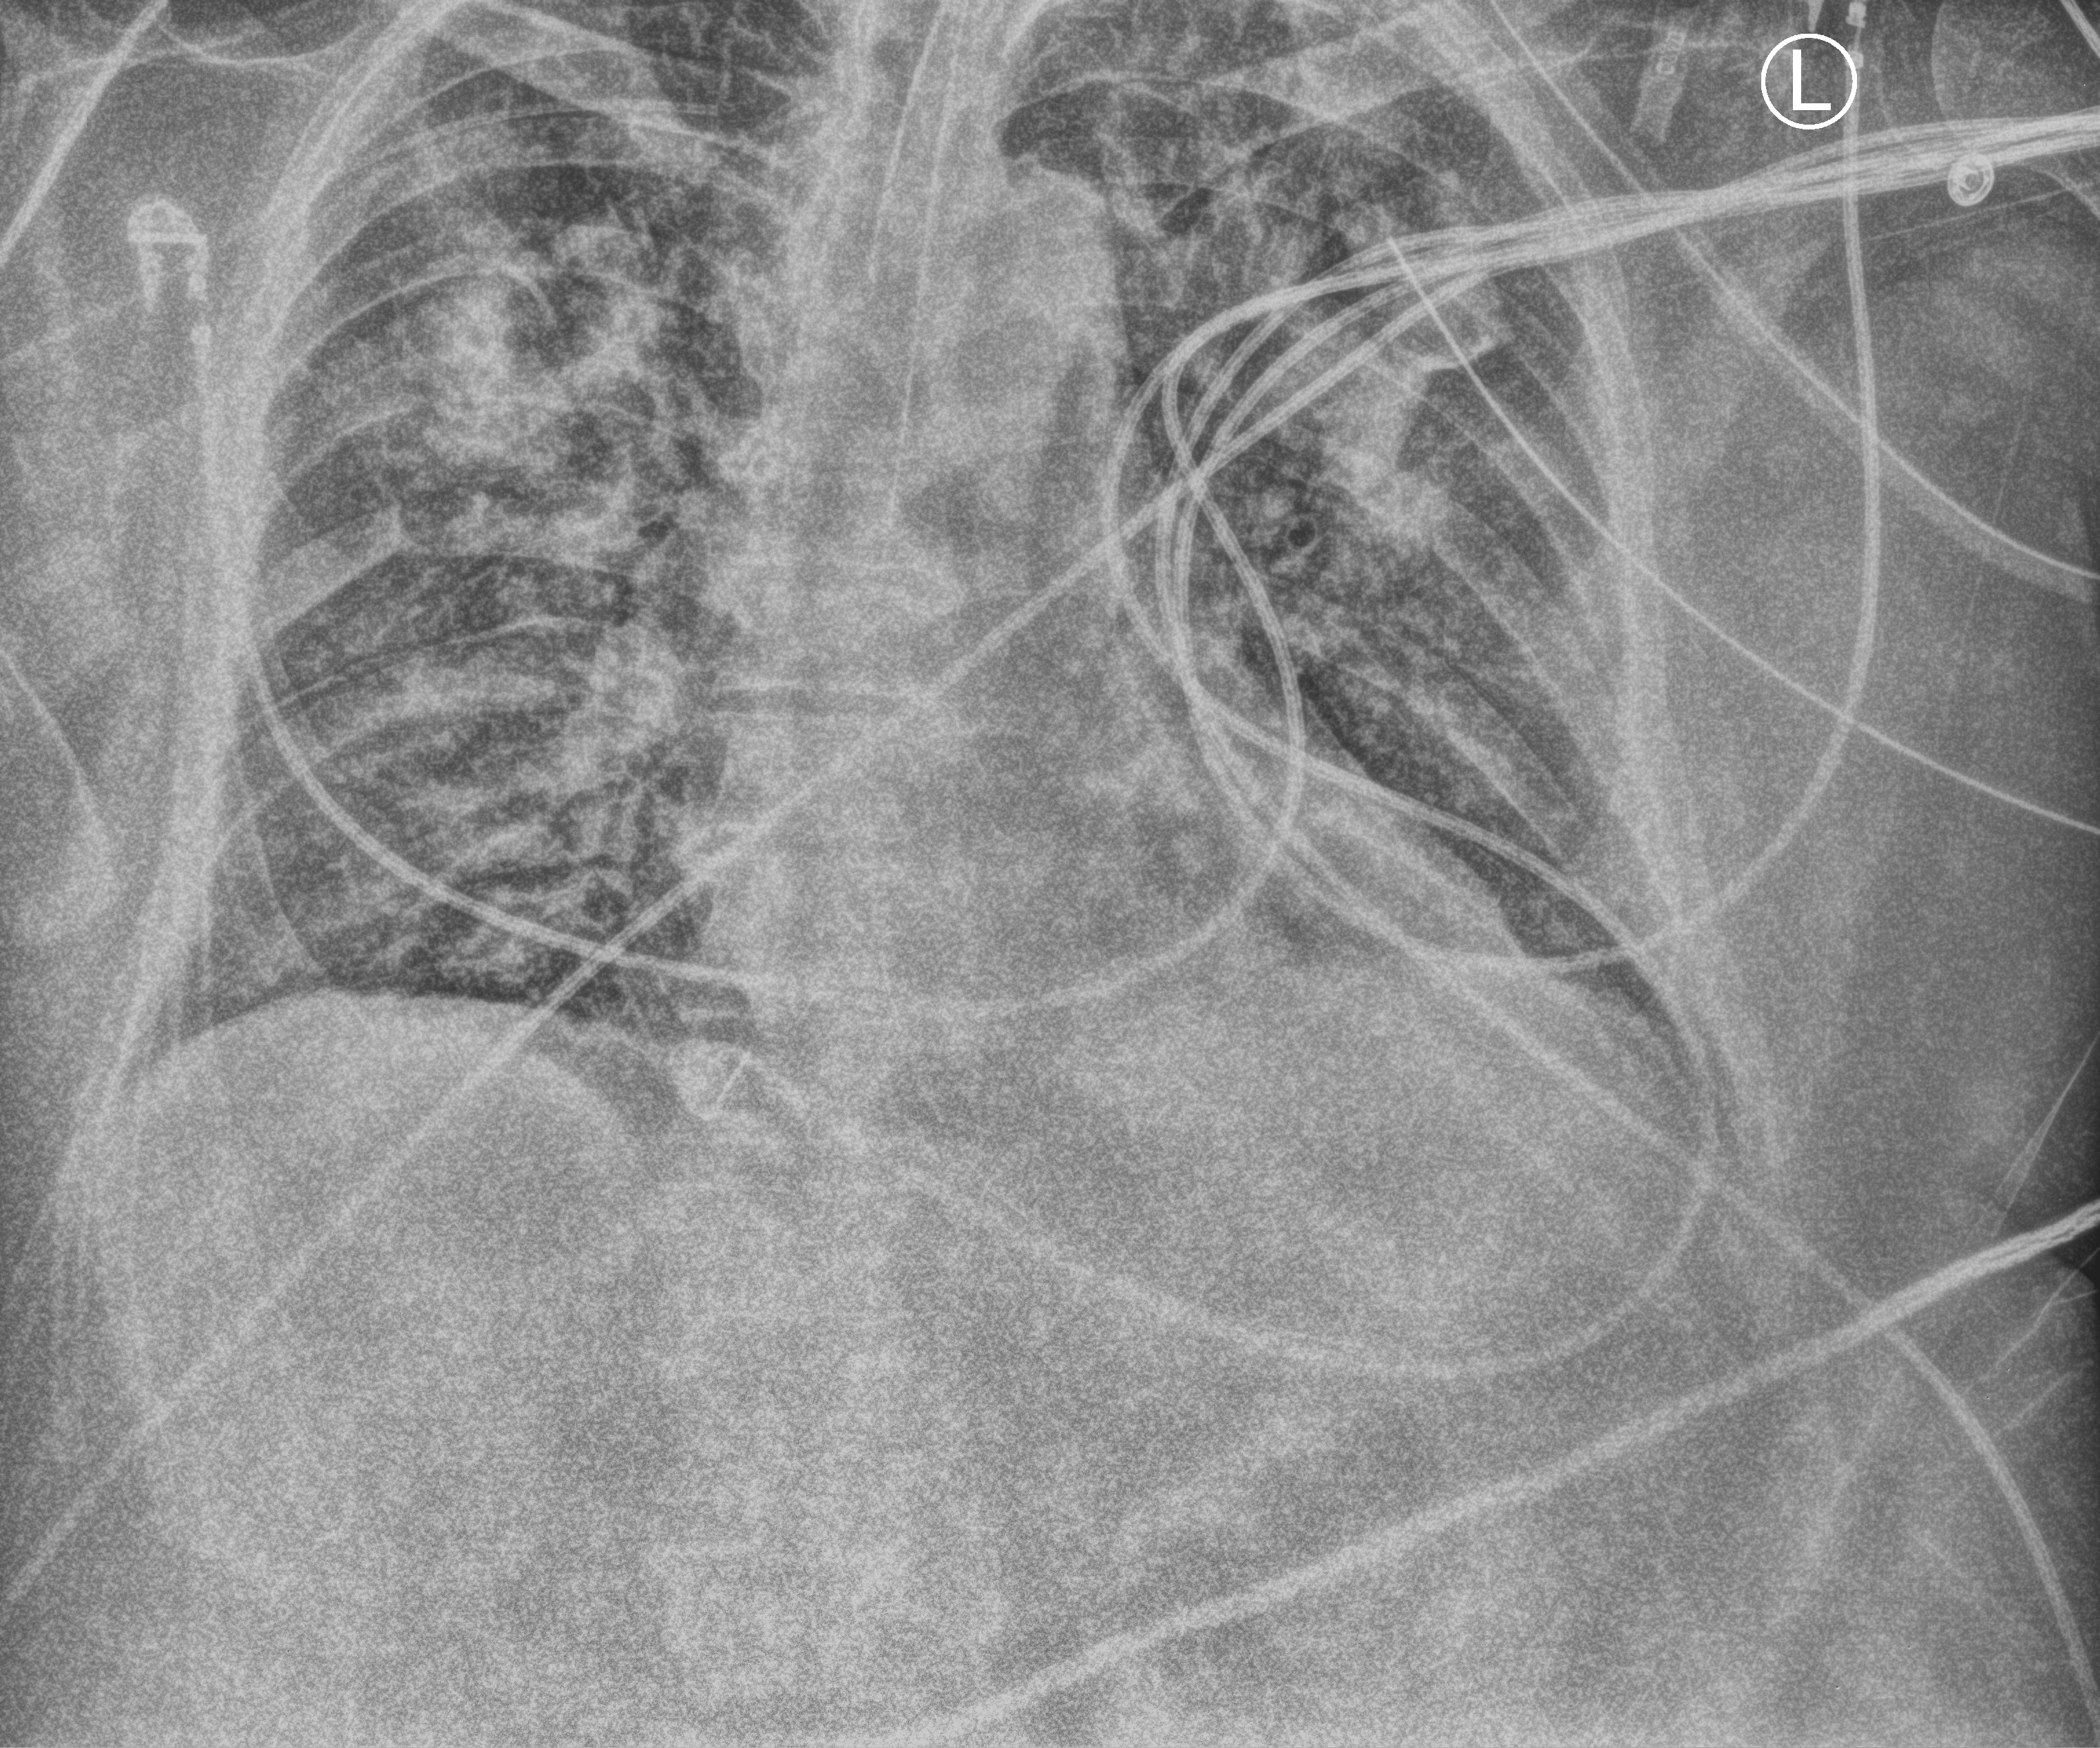
Chest X-ray (portable); anteroposterior (AP) projection. Male patient hospitalised with COVID-19, age 60–74 years.
Hospital-stay facts (about this admission, not read from this image; timing relative to this image not recorded): diabetes (admission record): no; admitted to intensive care during this hospital stay: yes.